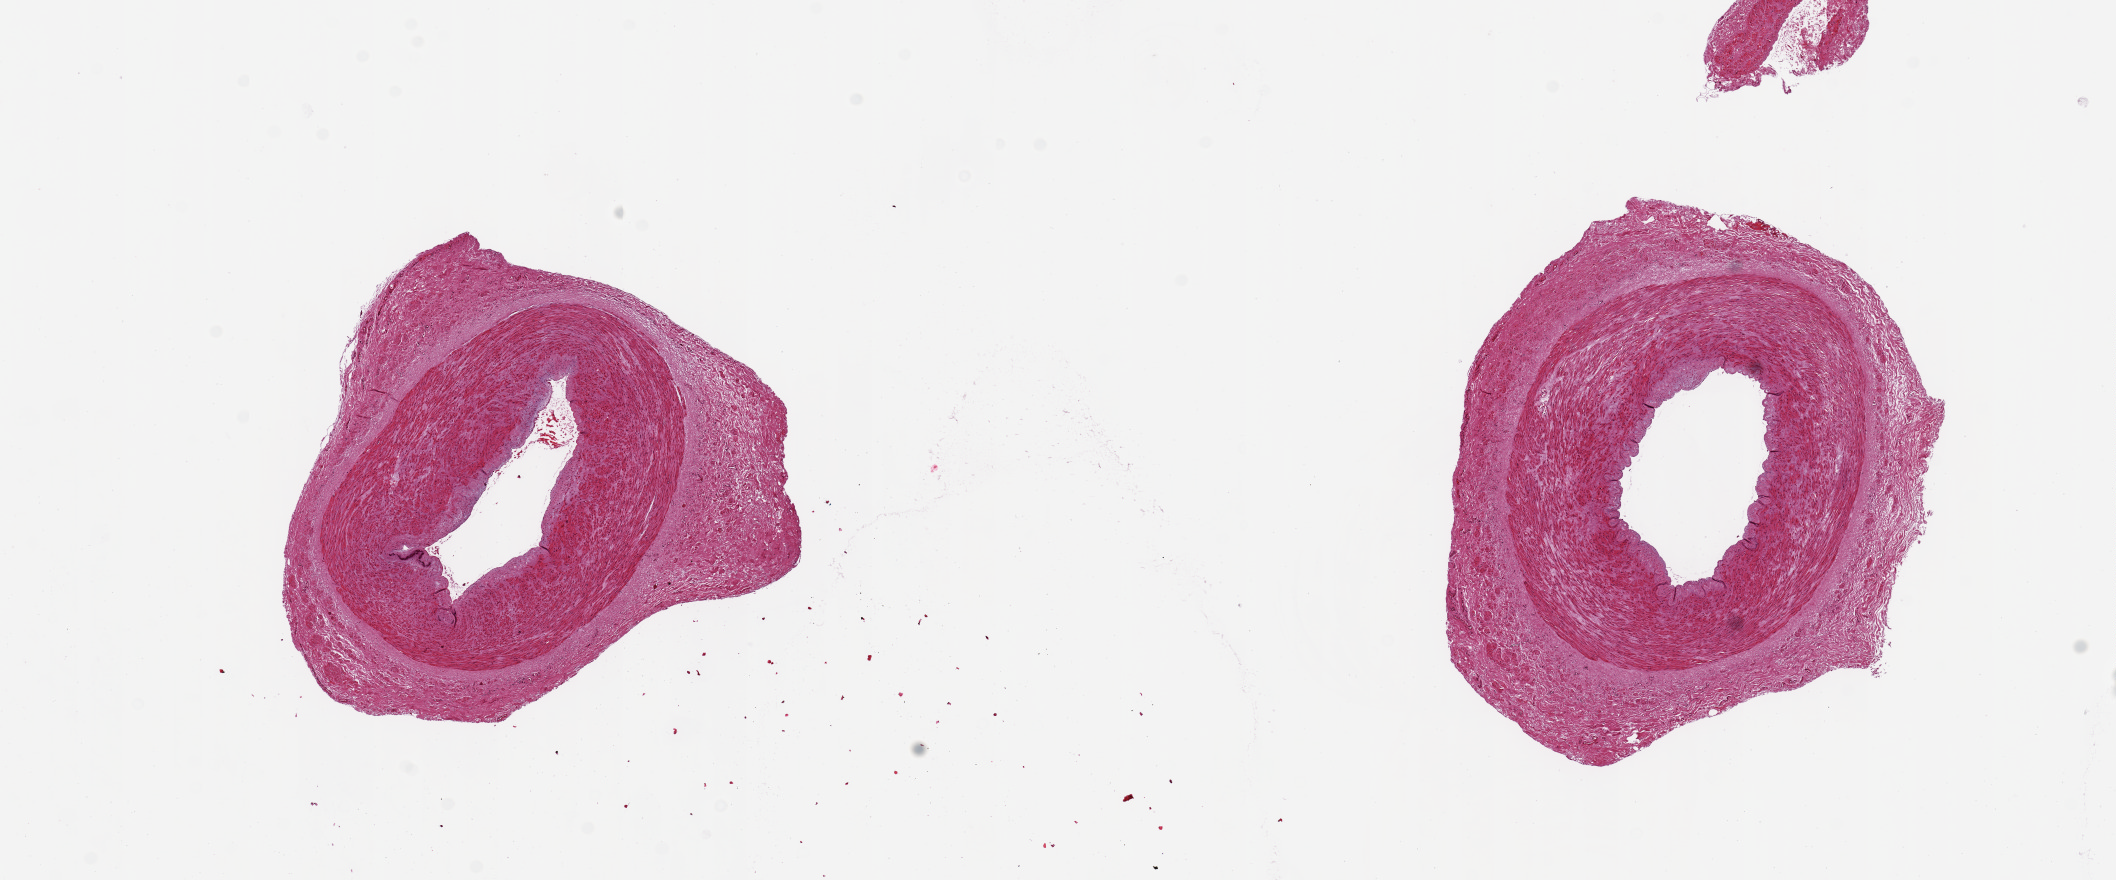
Digitized haematoxylin and eosin-stained section, brightfield, whole scanned area (about 16.7 x 7.0 mm, from a 20x scan) shown as a low-resolution overview, PAXgene-fixed, paraffin-embedded tissue, sampled site (target tissue): tibial artery, donor tissue sample. Donor: male.
Pathologist's review note for this sample: 2 pieces, 4x4 & 4x4mm; No lesions. Up to 1 mm concentric adventitial fibrous tissue.